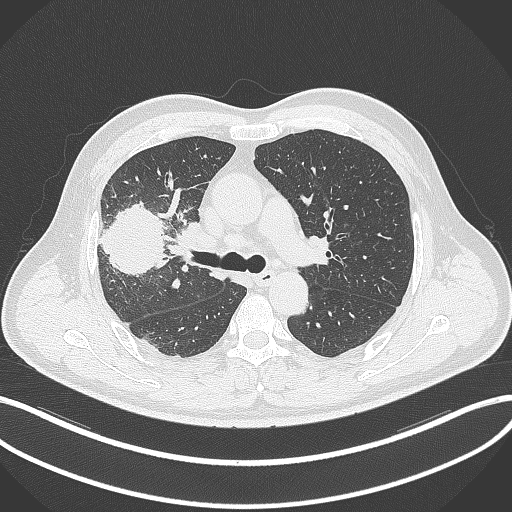
Chest CT, one axial slice; position 213 of 348 along the scan axis; lung window (W 1500 / L -600 HU); 1 mm slice thickness; 512 × 512 image matrix. Patient: male, 55 years. Case-level facts recorded for this patient, not image findings: clinical TNM (as recorded): T3 N2 M1.
Outlined on this slice (rectangle marked by the reading radiologist):
- lung tumour (recorded histology: adenocarcinoma): bounding box <100,199,175,276> (left, top, right, bottom; pixels)